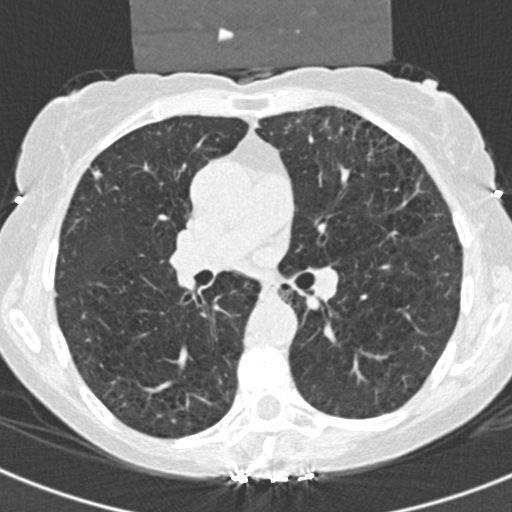
Low-dose screening chest CT, one axial slice. Position 109 of 181 along the scan axis. 120 kVp. Lung window (W 1500 / L -600 HU). 2 mm slice thickness. 512 × 512 image matrix, field of view 298 × 298 mm.
Annotated regions visible in this slice (expert manual segmentation):
- lesion 1 (tumor, upper lobe of right lung): bounding box (x1, y1, x2, y2) in pixels: (91, 169, 103, 179)